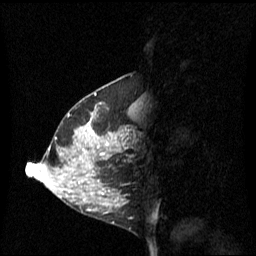
Breast MRI (dynamic contrast-enhanced), one sagittal slice; slice 25 of 60 in the series (ordered by position); dynamic contrast-enhanced series, image 2 of 3 at this slice position (ordered by acquisition); 1.5 T; TE 4.2 ms, TR 8.4 ms; 256 × 256 image matrix, field of view 240 × 240 mm. Patient: female, 42 years. Case-level facts recorded for this patient, not image findings: setting: breast cancer imaged before/during neoadjuvant chemotherapy; receptor status: HR-positive, HER2-negative.
Structures marked on this image (semi-automatic segmentation, software-assisted and operator-edited):
- analysis volume of interest (the breast-tissue region the enhancement analysis was run in; not a lesion): bounding box <68,102,137,201> (left, top, right, bottom; pixels)
- tumour enhancement mask (voxels above the 70 % enhancement threshold inside the analysis volume of interest): <88,114,109,145>